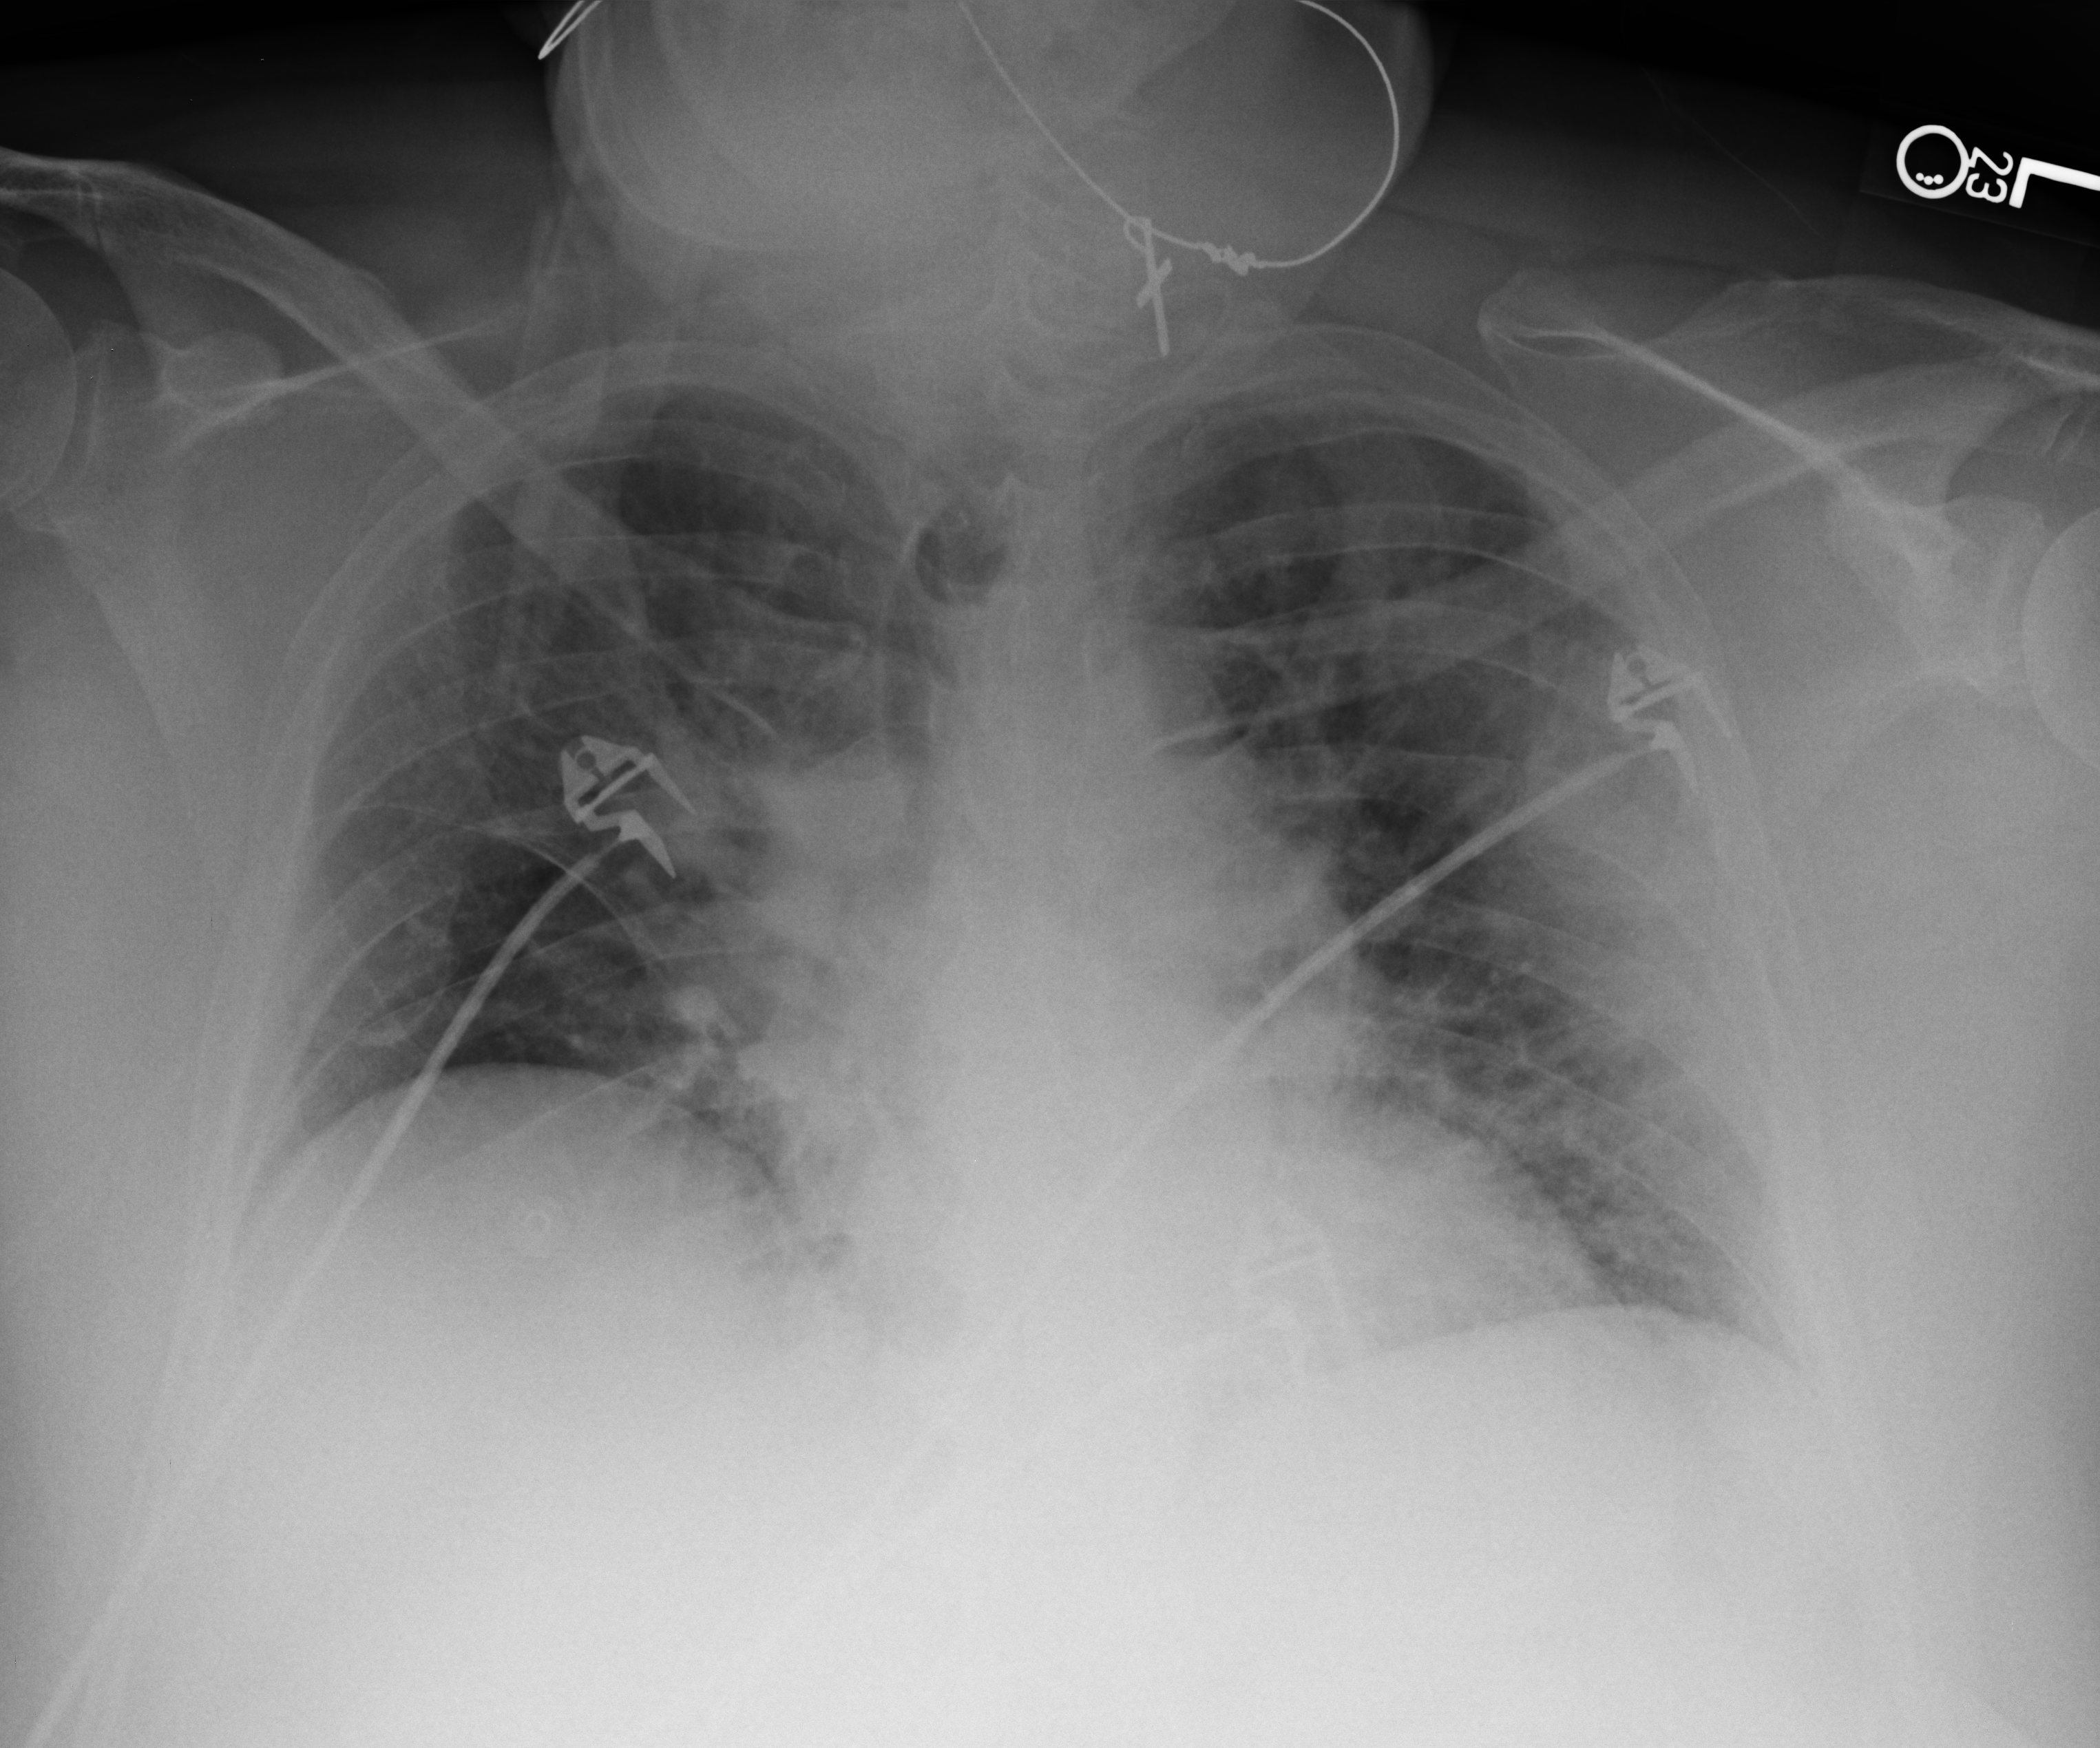
Portable chest radiograph; anteroposterior (AP) projection. Patient hospitalised with COVID-19; male, aged 60–74 years.
From the hospital-stay record, not from the radiograph (when in the stay this image was taken is not recorded):
- other chronic lung disease (admission record): no
- length of hospital stay: 11 days
- mechanically ventilated during this hospital stay: no